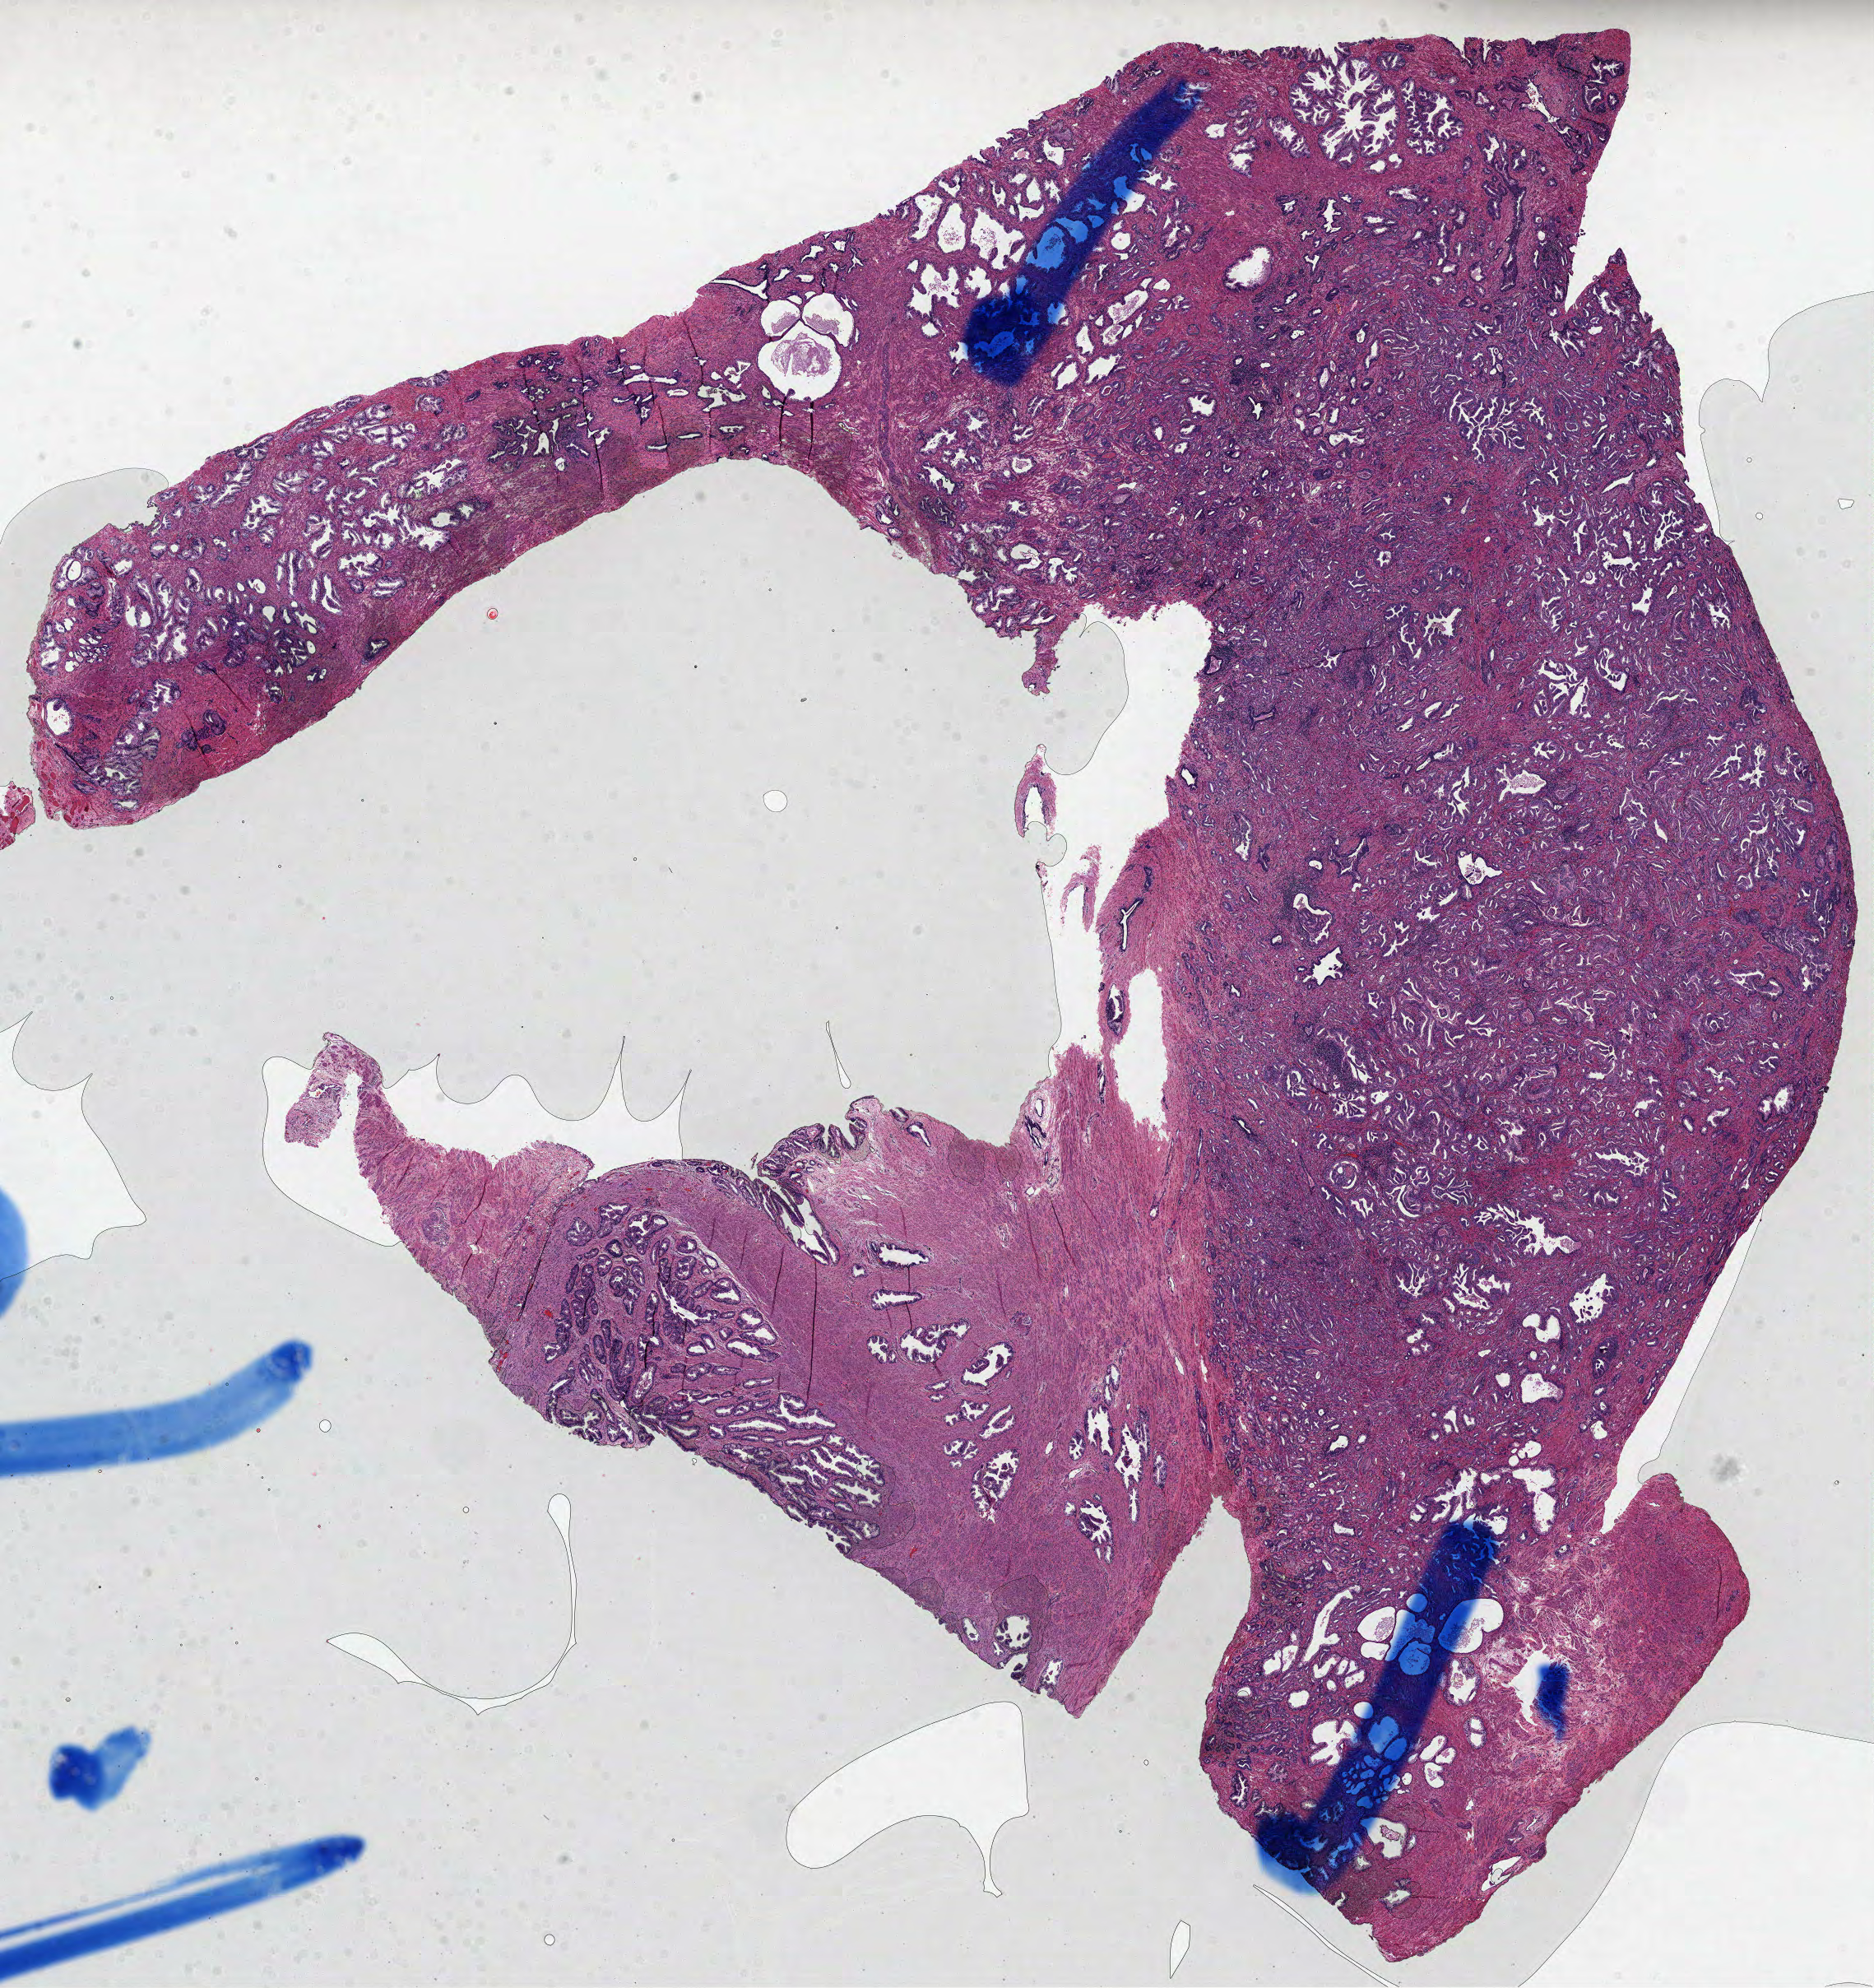
Whole-slide histology image, Hematoxylin and eosin (H&E) stained — low-resolution overview of the scanned area, about 18.4 x 19.5 mm (slide scanned at 40x). Formalin-fixed paraffin-embedded (FFPE) diagnostic section. Sample: primary tumour, prostate. Patient: male, age at initial diagnosis 51 years. Gleason score: 7 (3+4).
Lymph nodes positive (case pathology): 0 of 22 examined. Diagnosis: Acinar cell carcinoma. Laterality: bilateral.